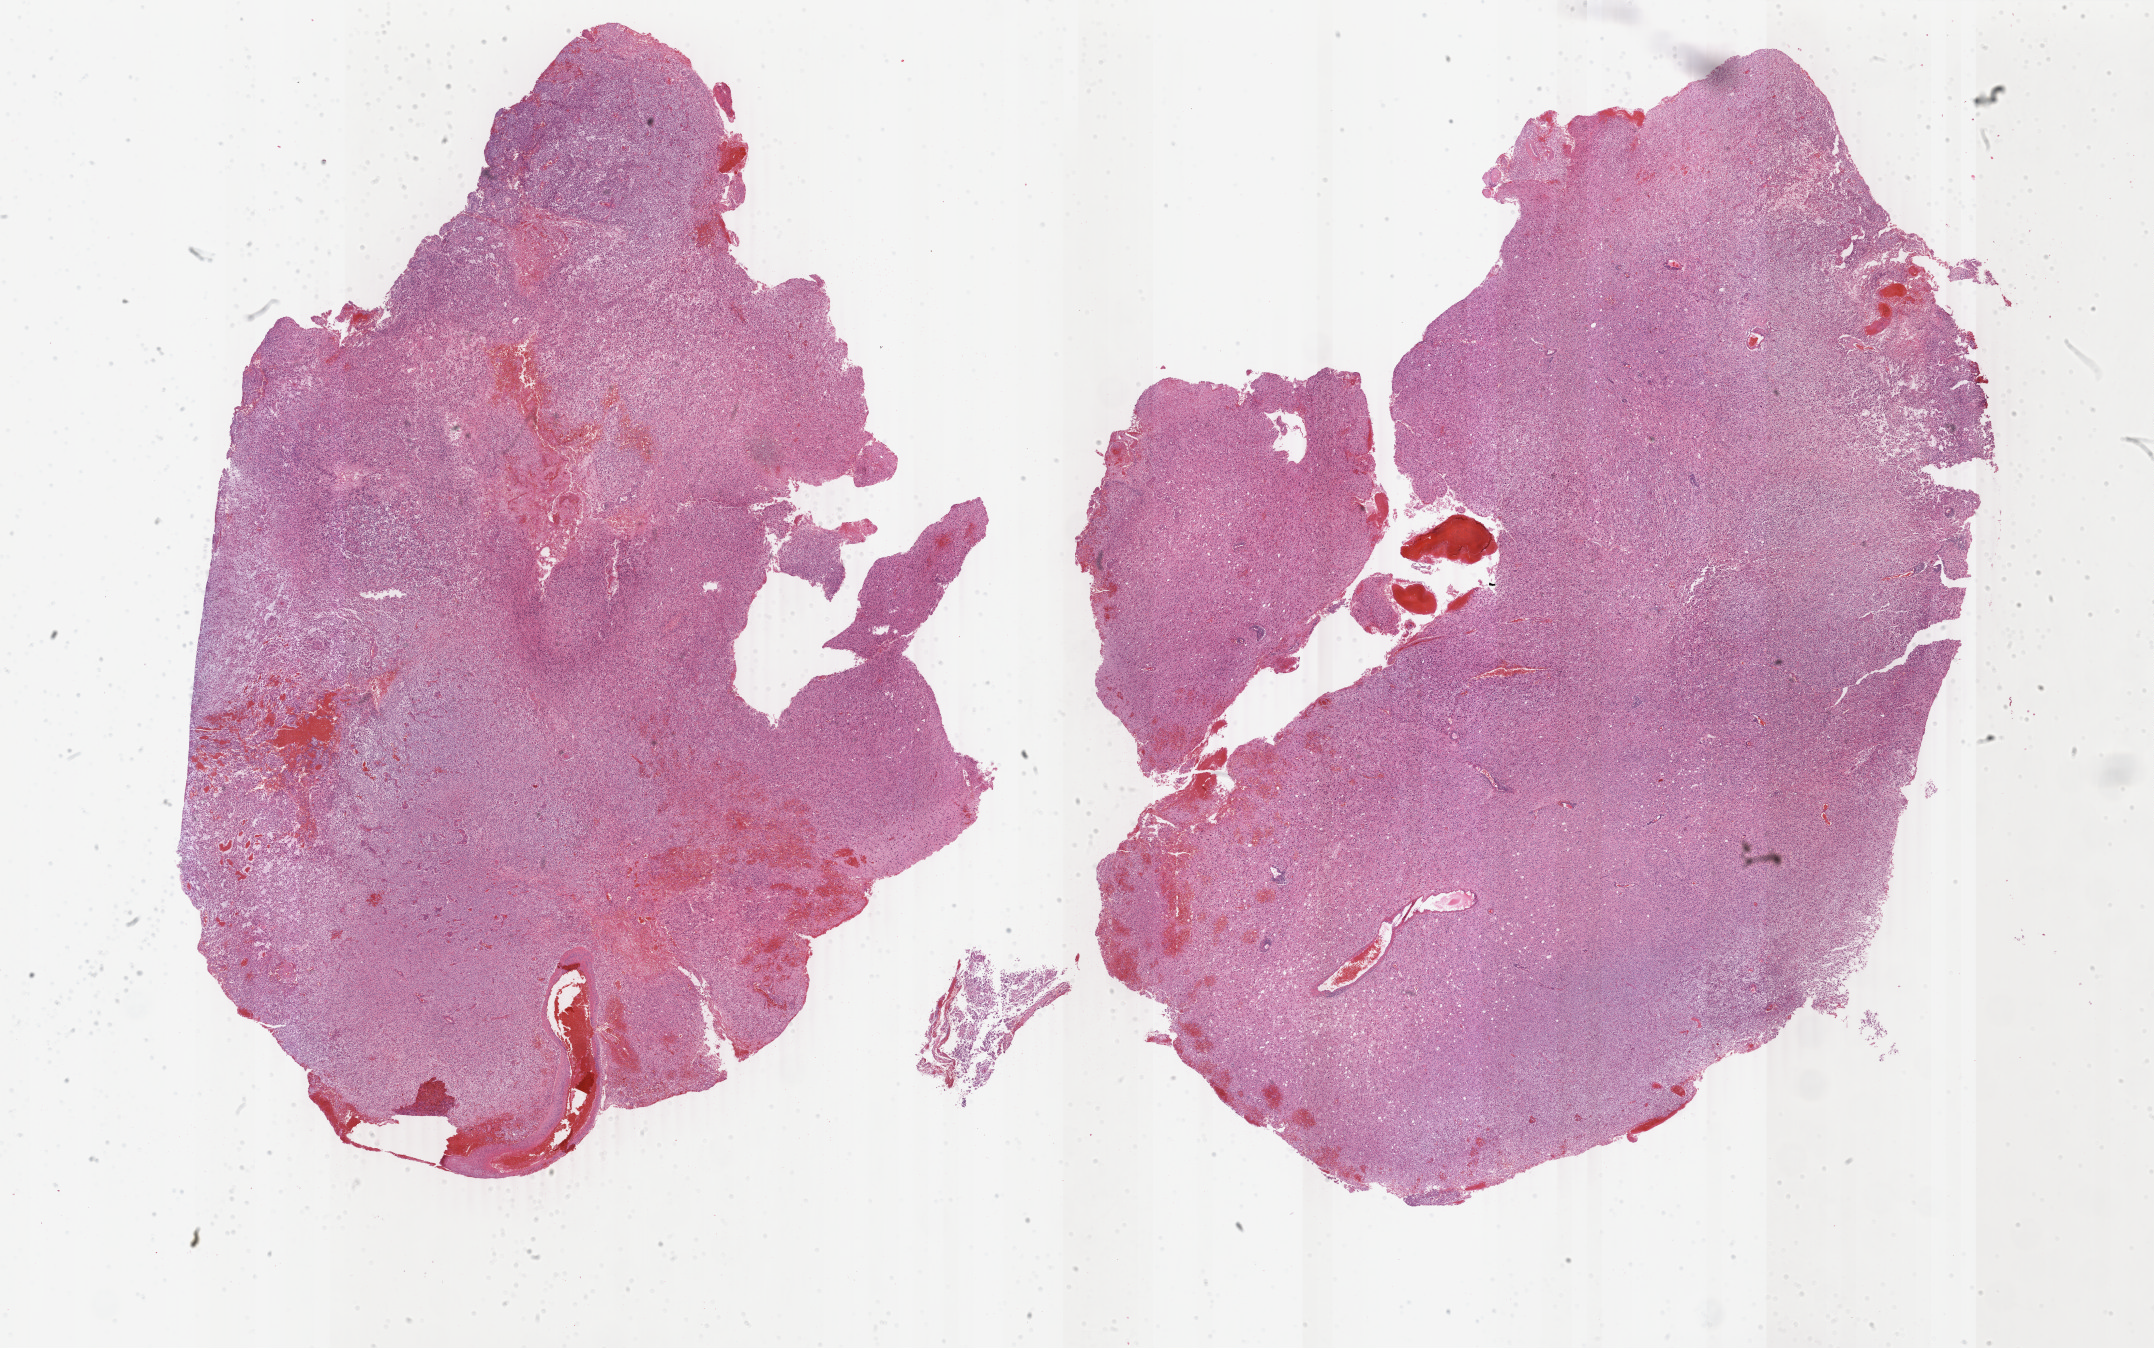
Whole-slide histology image, Hematoxylin and eosin (H&E) stained, shown as a low-resolution overview of the whole scanned area (about 34.3 x 21.4 mm); FFPE section; primary tumour sample from the brain. Male patient; age at initial diagnosis 70 years. Histologic grade: G3 (poorly differentiated).
Pathologic diagnosis: Oligodendroglioma, anaplastic (cerebrum).